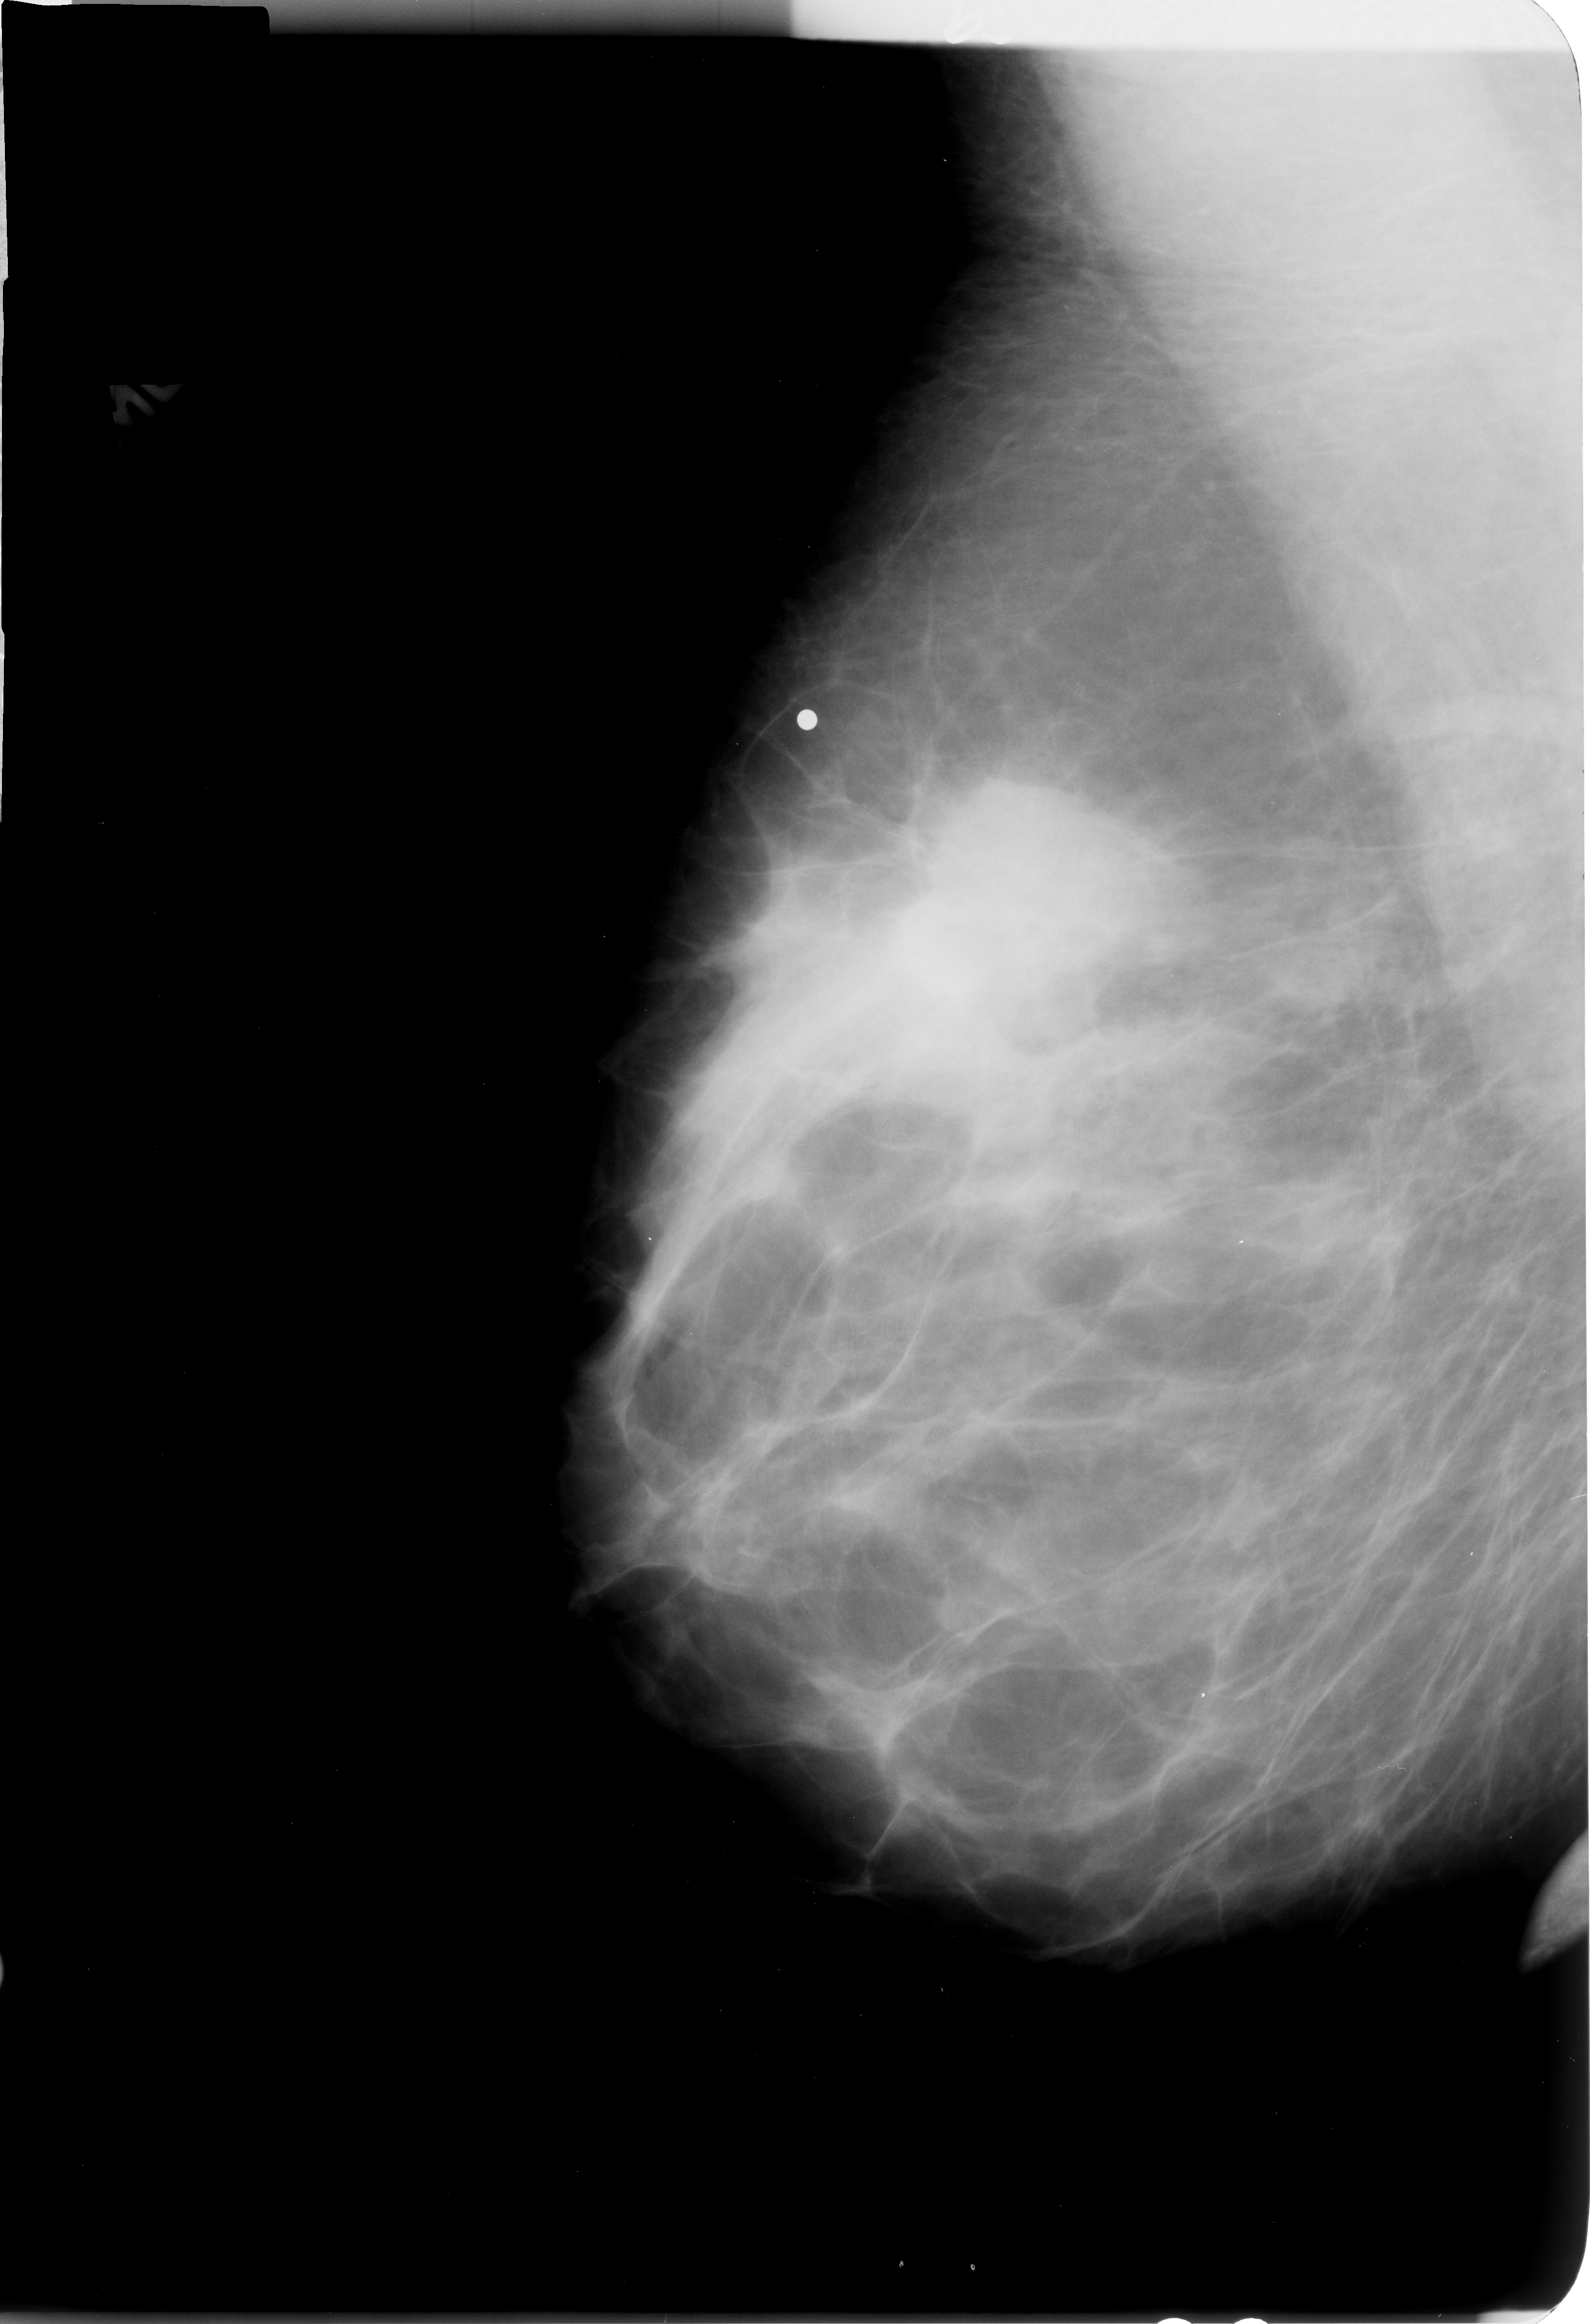
Digitized screen-film mammogram. Right breast. Mediolateral oblique (MLO) view. Breast composition: heterogeneously dense (BI-RADS density category 3 of 4). 1590 × 2324 image matrix.
Expert-marked regions of interest on this film, with their recorded descriptors:
- mass, shape irregular / architectural distortion, margins obscured / ill defined / spiculated; BI-RADS assessment category 4; pathology result (as recorded, not read from the image): malignant: bounding box [x1, y1, x2, y2] px = [731, 752, 1124, 1123]